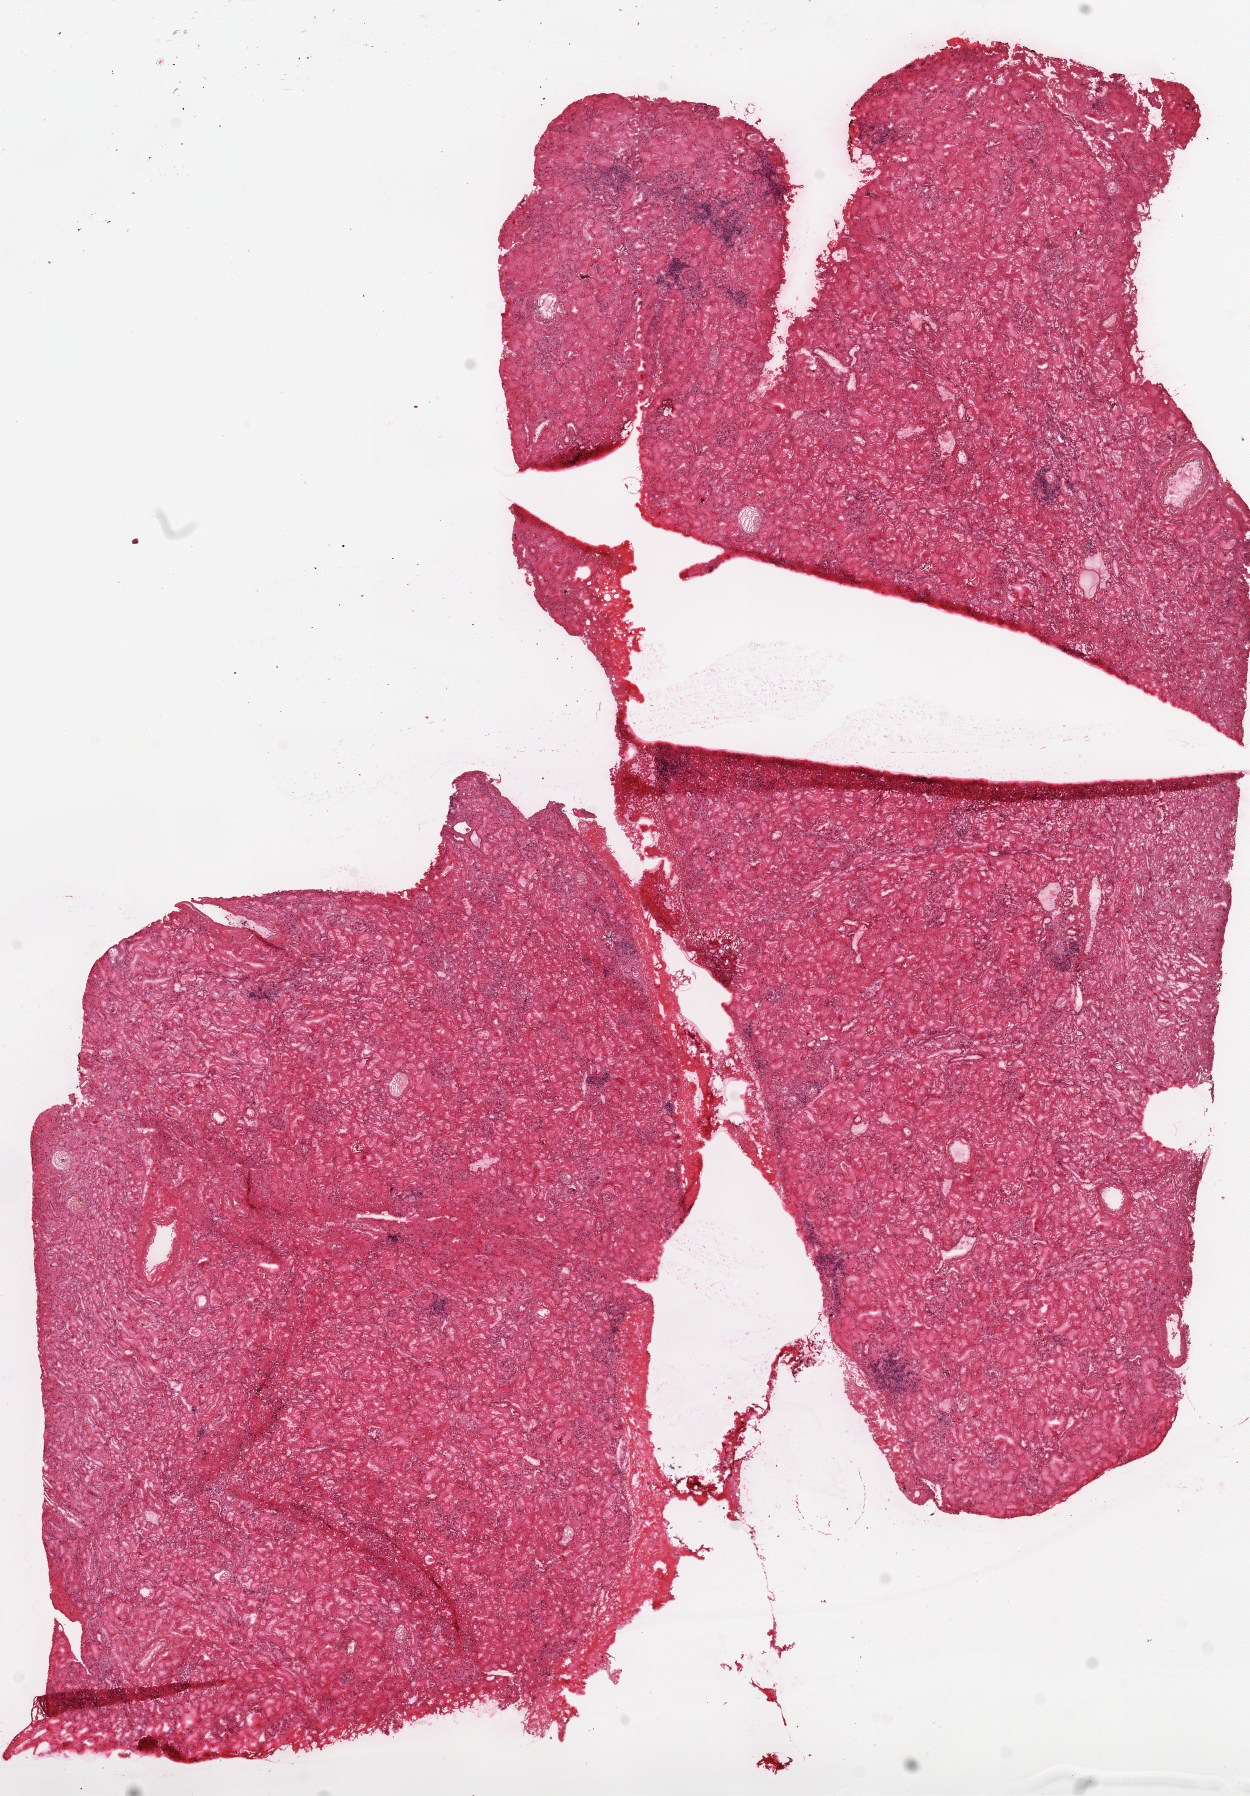
Whole-slide histology image, H&E-stained — shown as a low-resolution overview of the whole scanned area (about 10.0 x 14.4 mm, slide scanned at 20x); frozen section from the top of the tissue portion; kidney, solid tissue normal (non-tumour tissue) sample. Patient: male, age at initial diagnosis 54 years.
• this section: solid tissue normal sample (biorepository sample class)
• patient diagnosis: Clear cell adenocarcinoma, NOS